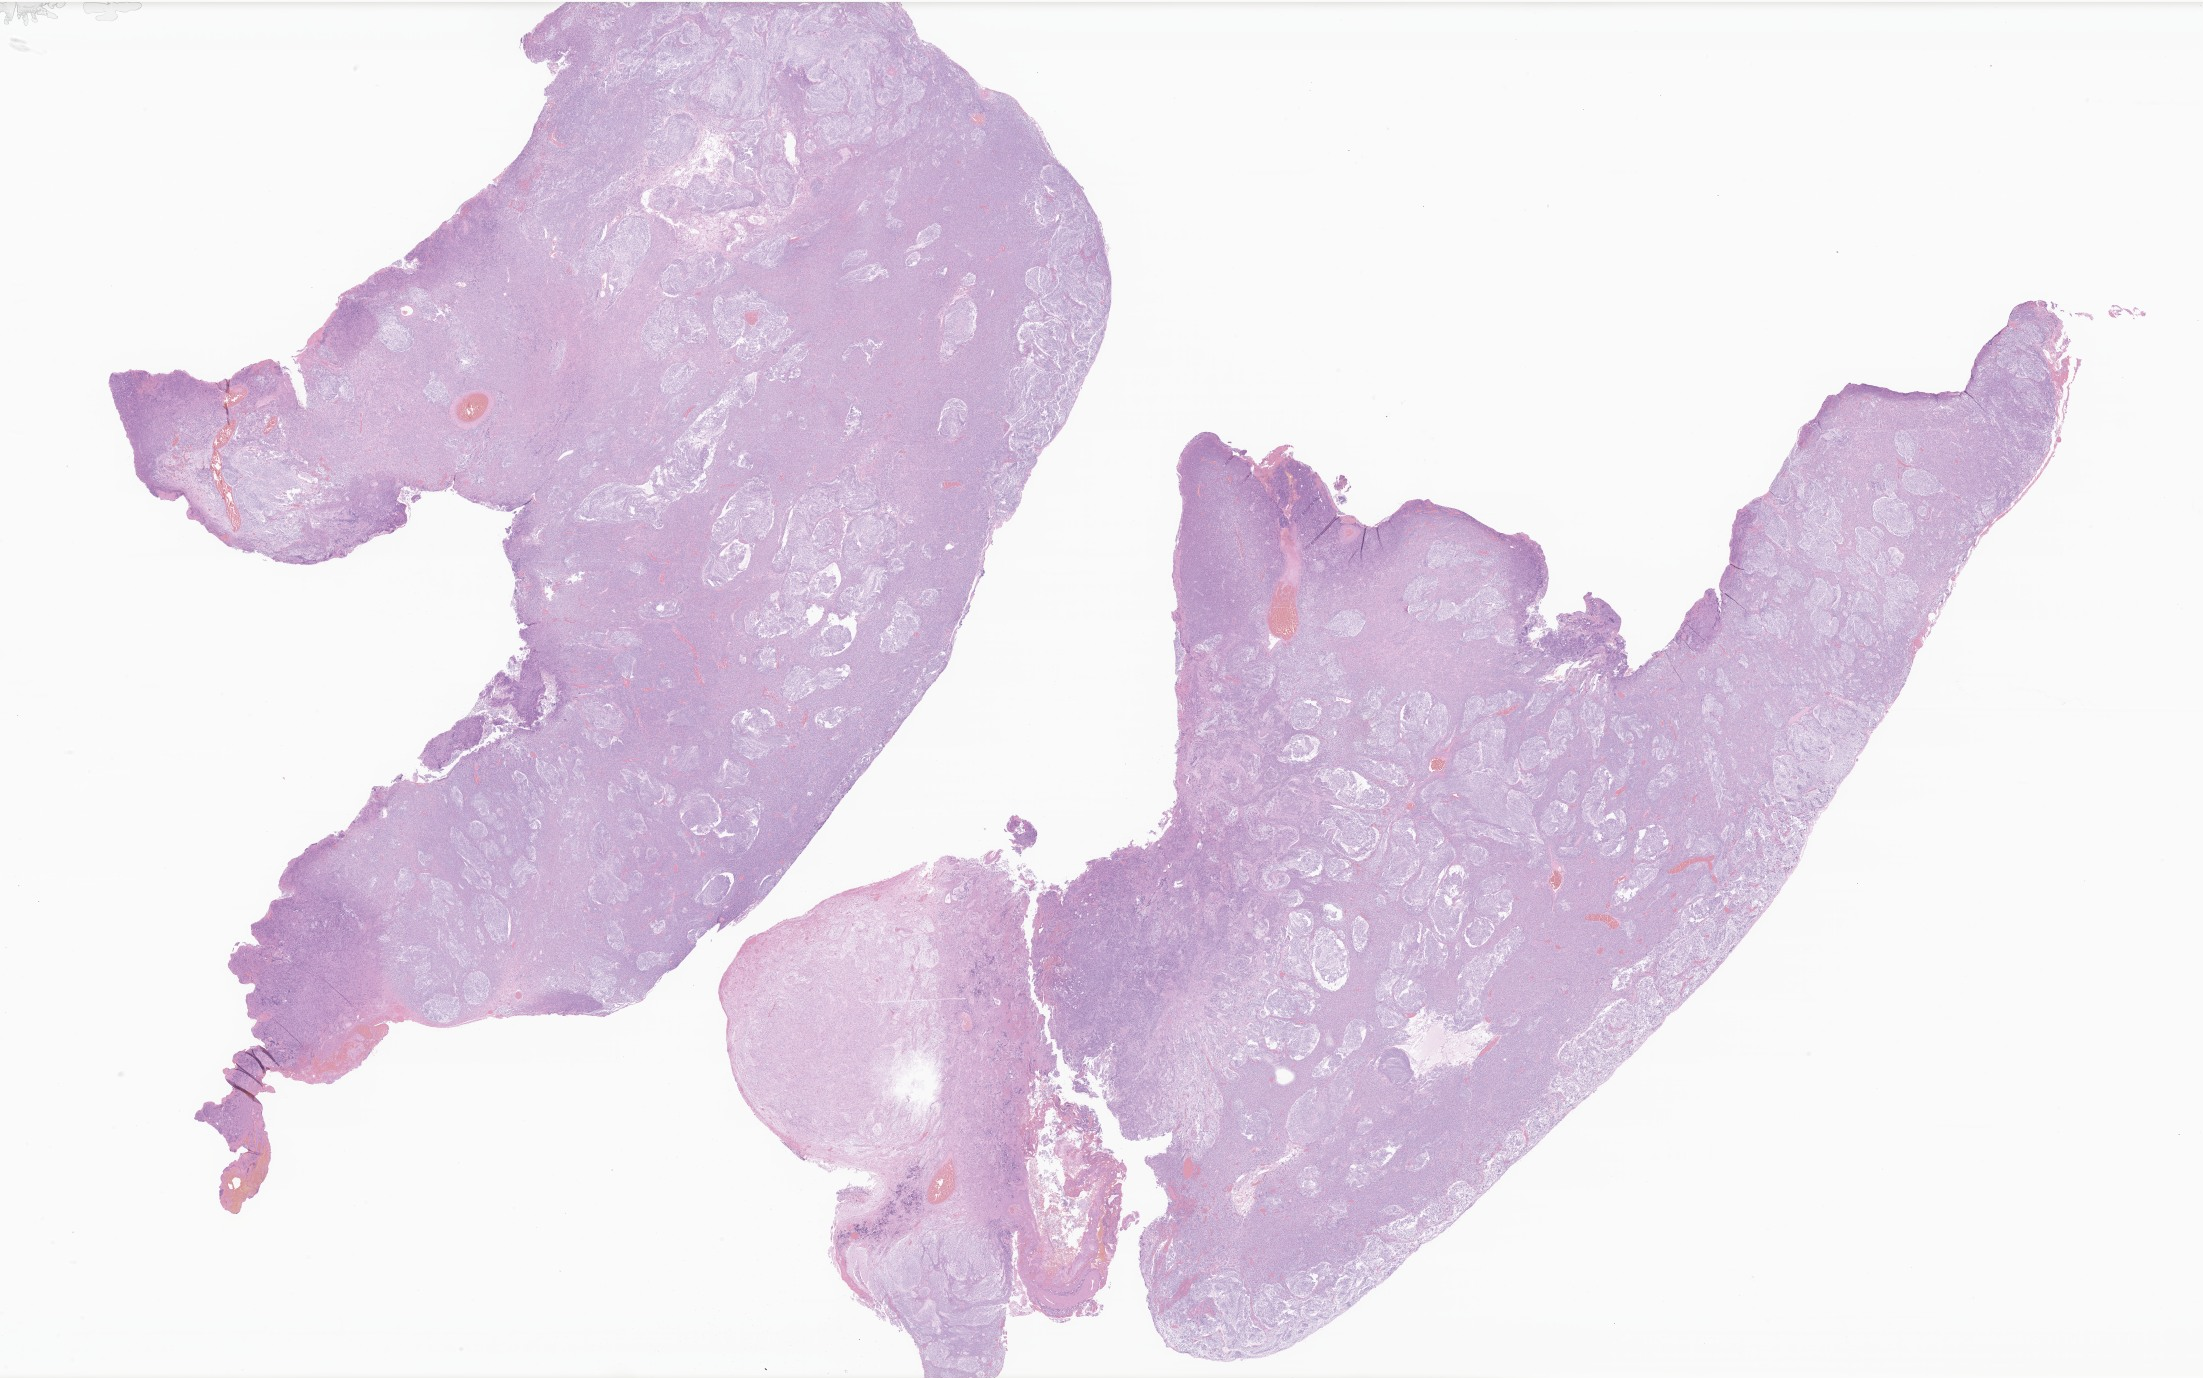
Whole-slide image, hematoxylin and eosin (H&E) stain of tumor tissue from the brain, low-resolution overview of the scanned area, about 37.1 x 23.2 mm, formalin-fixed paraffin-embedded section. Patient female; age 754 days (about 2.1 years).
Recorded diagnosis: Neoplasm, uncertain whether benign or malignant.